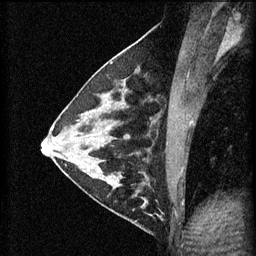
Breast MRI (dynamic contrast-enhanced), one sagittal slice. Slice 28 of 60 in the series (ordered by position). 3 images stored at this slice position (order not interpretable as contrast timing). 1.5 T. TE 4.2 ms, TR 11 ms. 256 × 256 image matrix, field of view 180 × 180 mm. Female patient, age 29 years.
Outlined on this slice (semi-automatically segmented with operator editing):
- analysis volume of interest (the breast-tissue region the enhancement analysis was run in; not a lesion): bounding box [x1, y1, x2, y2] px = [105, 172, 171, 227]
- tumour enhancement mask (voxels above the 70 % enhancement threshold inside the analysis volume of interest): [108, 172, 162, 217]